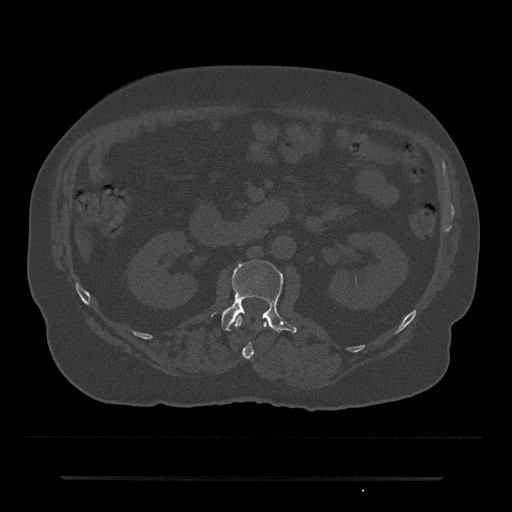
CT including the spine, one axial slice. Slice 26 of 797 in the series (ordered by position). Bone window (W 1800 / L 400 HU). 0.5 mm slice thickness. 512 × 512 image matrix, field of view 437 × 437 mm. Male patient, age 69 years. Case-level facts recorded for this patient, not image findings: primary cancer: prostate.
Annotated regions visible in this slice (semi-automatically segmented with operator editing):
- L1 vertebra: bounding box <234,315,267,359> (left, top, right, bottom; pixels)
- L2 vertebra: <221,260,297,333>